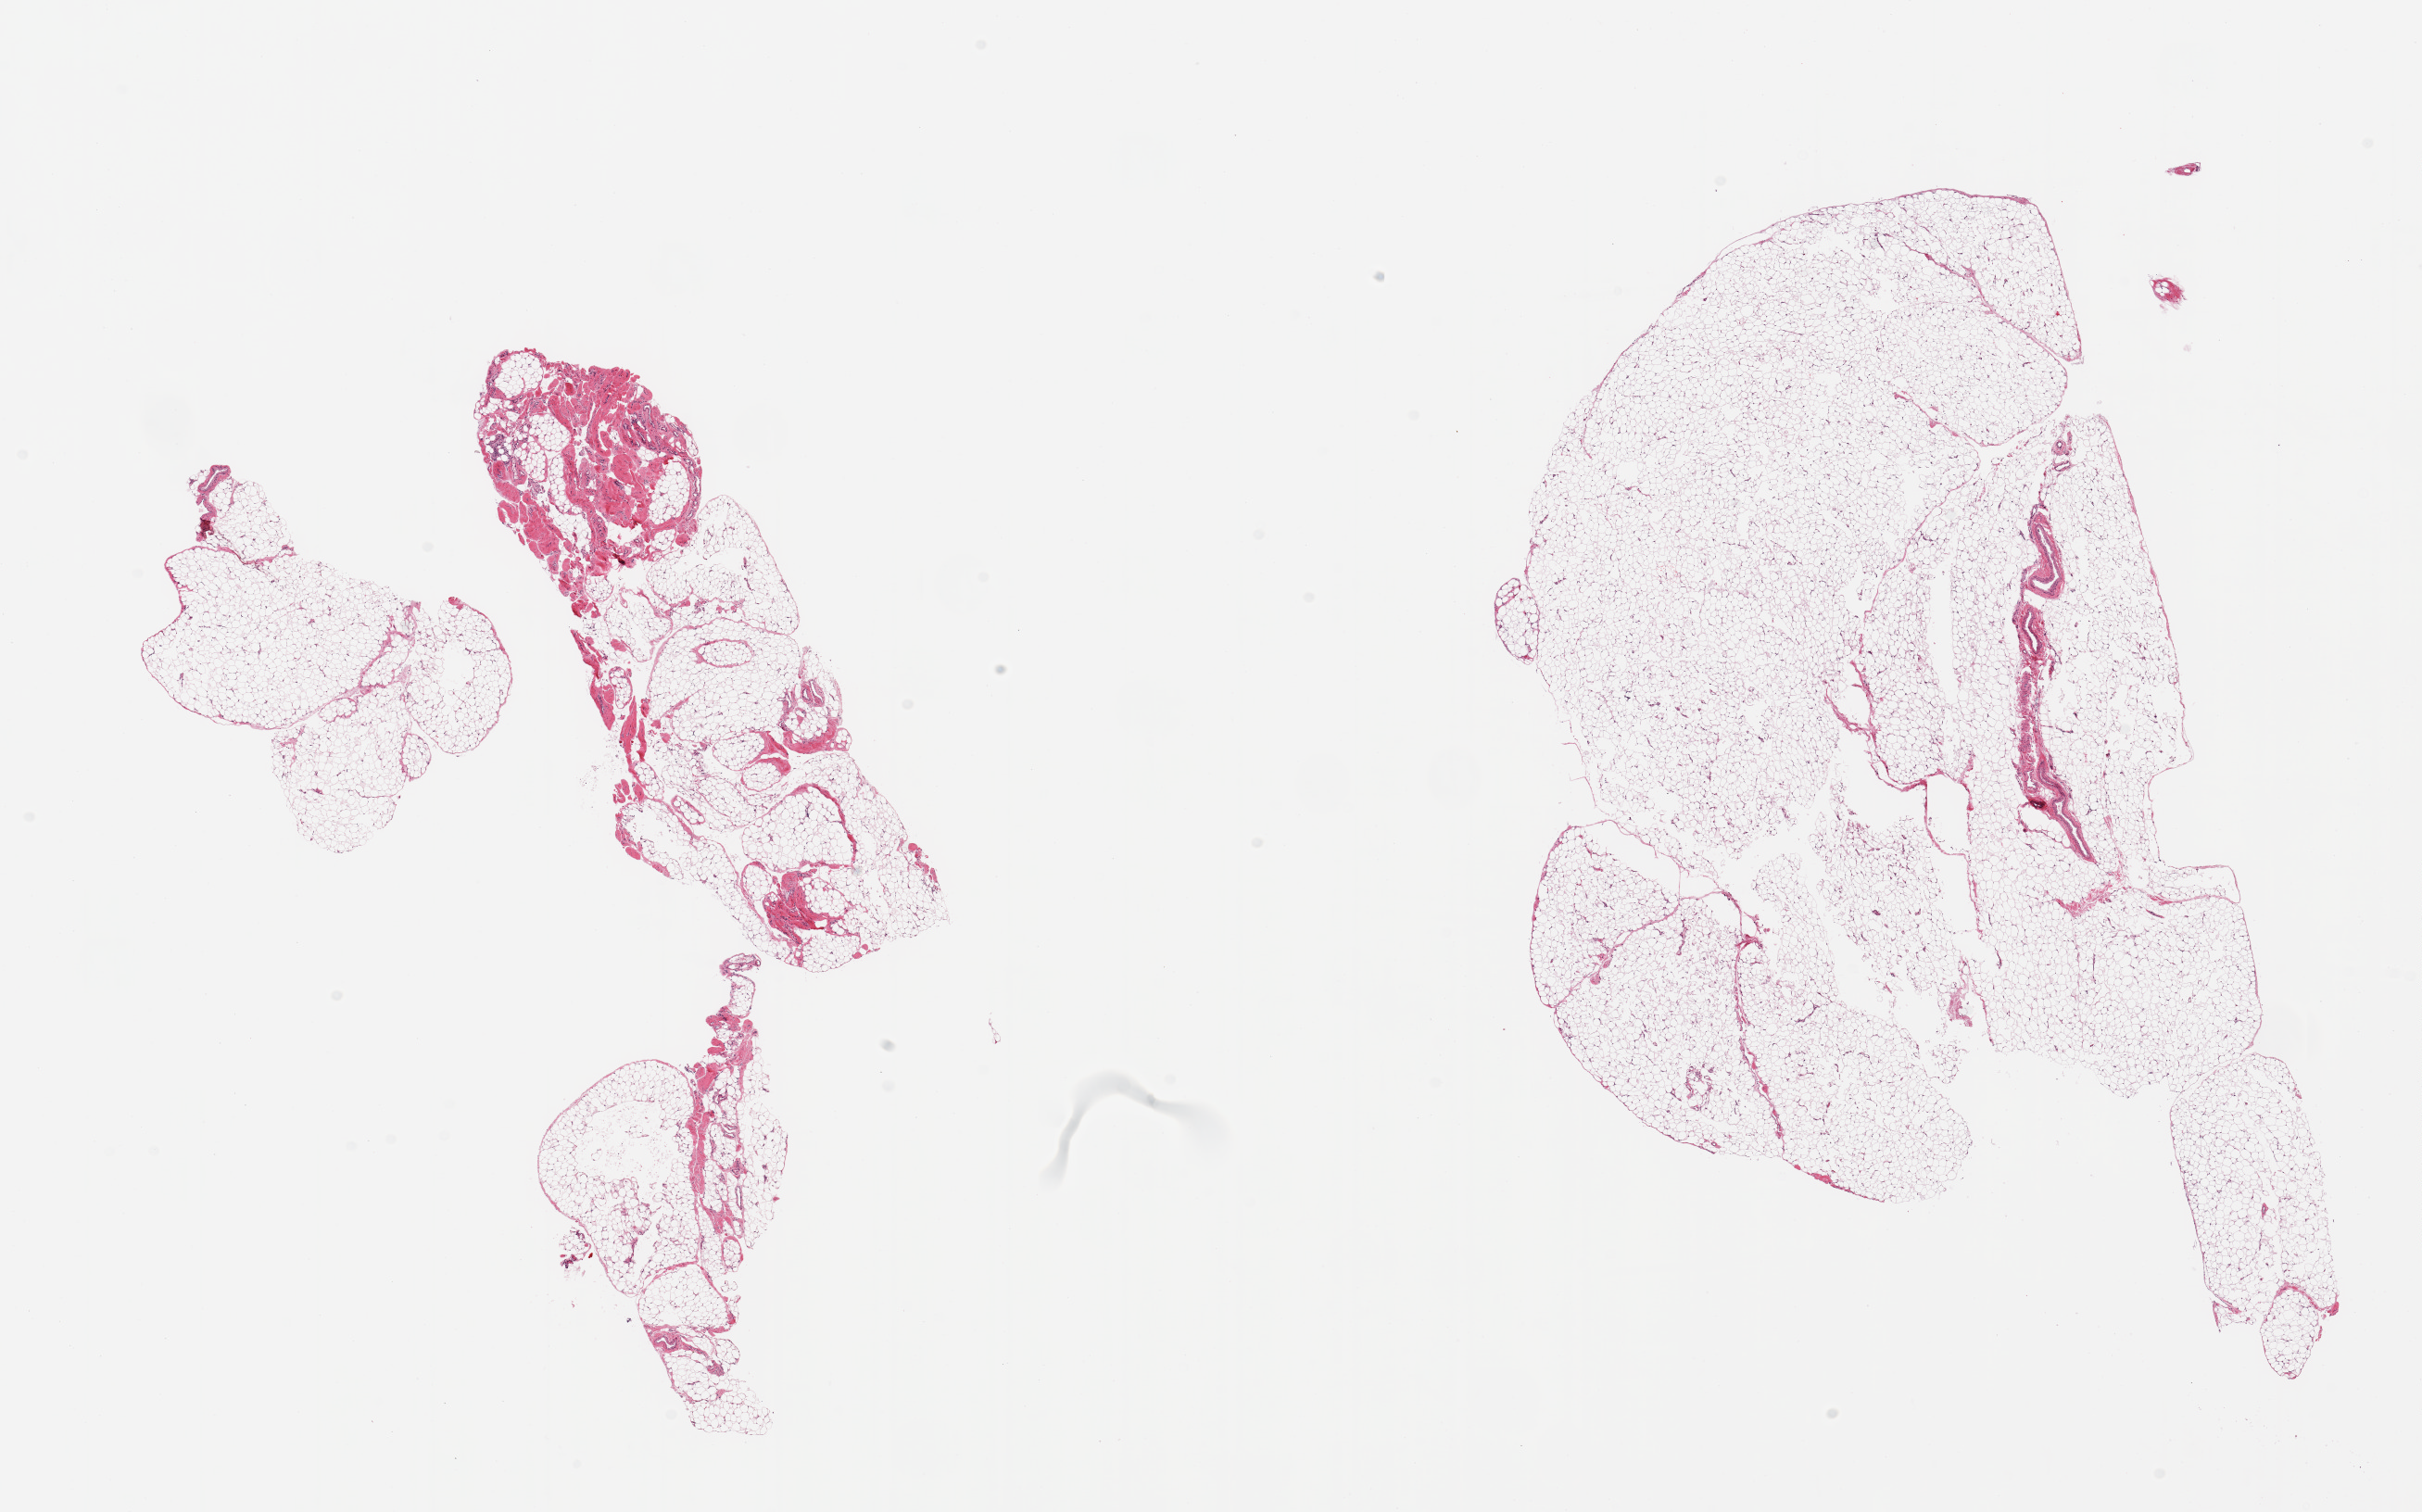
Digitized hematoxylin and eosin (H&E)-stained section, brightfield — whole scanned area (about 20.7 x 12.9 mm, slide scanned at 20x) shown as a low-resolution overview; PAXgene-fixed paraffin-embedded (PFPE) section; target tissue: omentum; tissue donor sample.
Reviewer comment on this tissue sample: 2 pieces, ~15-20% fascia/vascular elements.